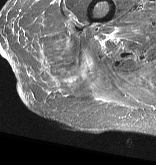
MRI of an extremity soft-tissue mass, one axial slice; position 13 of 57 along the scan axis; STIR; MR volume resampled by the dataset authors to the PET/CT grid (not the native acquisition matrix); 3.27 mm slice thickness; 156 × 165 image matrix, field of view 152 × 161 mm. Female patient. From the clinical record (not read from this slice): histological type: epithelioid sarcoma with vascular differentiation; site of the primary tumour: right buttock.
Annotated regions visible in this slice (expert contour drawn on MRI and transferred to this co-registered scan by the dataset authors):
- gross tumour volume (mass): bounding box [x1, y1, x2, y2] px = [40, 25, 86, 93]